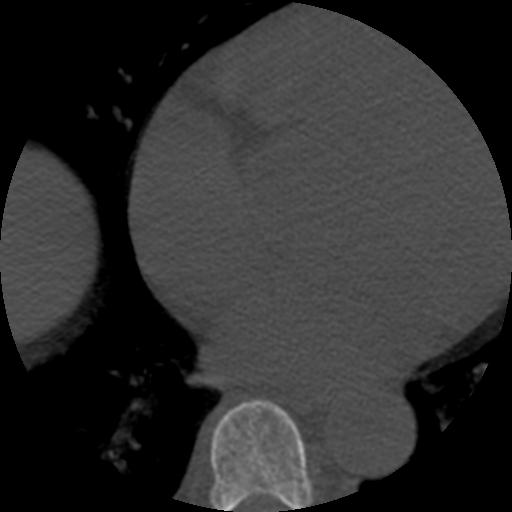
CT including the spine, one axial slice. Reconstruction kernel STANDARD. 120 kVp. Bone window (W 1800 / L 400 HU). 1.25 mm slice thickness. 512 × 512 image matrix. Patient age 57 years. From the clinical record (not read from this slice): primary cancer: prostate.
Annotated regions visible in this slice (semi-automatic segmentation, software-assisted and operator-edited):
- T7 vertebra: bounding box [x1, y1, x2, y2] px = [210, 400, 313, 512]